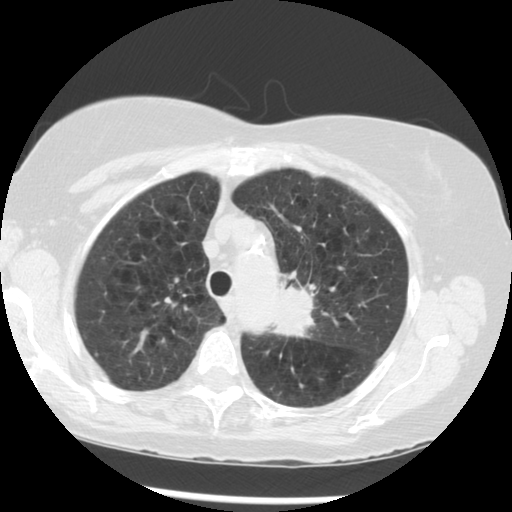
Low-dose screening chest CT, one axial slice; slice 217 of 283 in the series (ordered by position); 120 kVp; lung window (W 1500 / L -600 HU); 512 × 512 image matrix, field of view 330 × 330 mm.
Annotated regions visible in this slice (expert manual segmentation):
- lesion 1 (tumor, upper lobe of left lung): bounding box <272,285,313,337> (left, top, right, bottom; pixels)